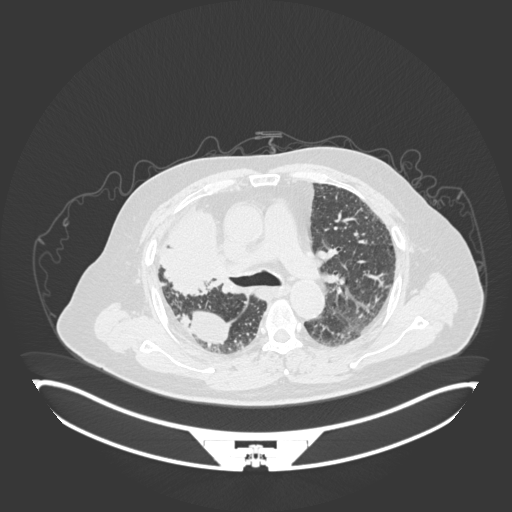
Chest CT, one axial slice. Position 115 of 201 along the scan axis. Reconstruction kernel B30f. Lung window (W 1500 / L -600 HU). 1 mm slice thickness. 512 × 512 image matrix. Male patient, age 69 years. Case-level facts recorded for this patient, not image findings: clinical TNM (as recorded): T4 N3 M1.
Annotated regions visible in this slice (rectangle marked by the reading radiologist):
- lung tumour (recorded histology: adenocarcinoma): bounding box <154,207,223,295> (left, top, right, bottom; pixels)